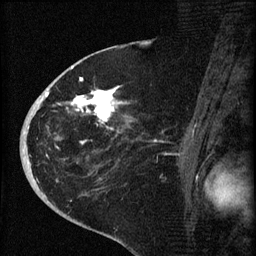
Breast MRI (dynamic contrast-enhanced), one sagittal slice; position 36 of 60 along the scan axis; dynamic contrast-enhanced series, image 2 of 4 at this slice position (ordered by acquisition); 1.5 T; TE 4.2 ms, TR 8.2 ms; 2 mm slice thickness; 256 × 256 image matrix, field of view 180 × 180 mm. Female patient, age 71 years.
Annotated regions visible in this slice (semi-automatically segmented with operator editing):
- analysis volume of interest (the breast-tissue region the enhancement analysis was run in; not a lesion): bounding box <35,75,142,190> (left, top, right, bottom; pixels)
- tumour enhancement mask (voxels above the 70 % enhancement threshold inside the analysis volume of interest): <38,77,122,144>